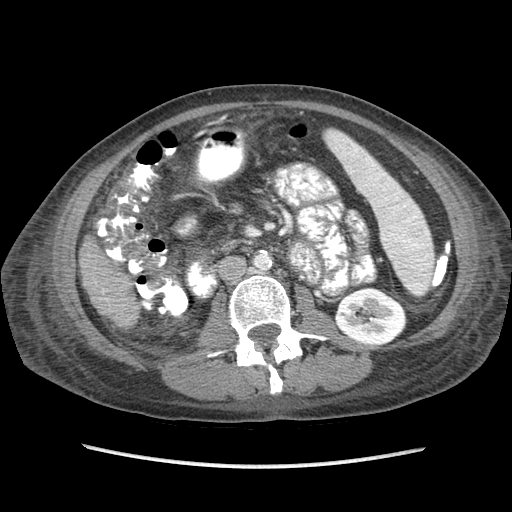
Contrast-enhanced abdominal CT (liver protocol), one axial slice; position 20 of 87 along the scan axis; 120 kVp; soft-tissue window (W 400 / L 40 HU); 2.5 mm slice thickness; 512 × 512 image matrix, field of view 340 × 340 mm. From the clinical record (not read from this slice): diagnosis: hepatocellular carcinoma (patient treated with transarterial chemoembolisation; whether this scan precedes or follows treatment is not stated here); TNM stage (as recorded): Stage-IIIB; Child-Pugh class: A; tumour differentiation: no biopsy; tumour nodularity: uninodular.
Structures marked on this image (semi-automatically segmented with operator editing):
- liver parenchyma outside the tumour (the mass and vessels are separate outlines, so this box may not span the whole liver): box from (x=80, y=234) to (x=138, y=326) px